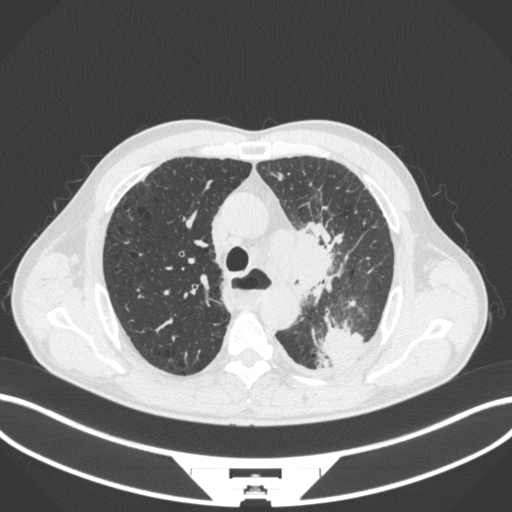
Chest CT, one axial slice; slice 274 of 411 in the series (ordered by position); reconstruction kernel B31f; lung window (W 1500 / L -600 HU); 1 mm slice thickness; 512 × 512 image matrix, field of view 400 × 400 mm. Patient: male, 57 years. Case-level facts recorded for this patient, not image findings: clinical TNM (as recorded): T2a N1 M0.
Outlined on this slice (rectangle marked by the reading radiologist):
- lung tumour (recorded histology: squamous cell carcinoma): bounding box [x1, y1, x2, y2] px = [262, 220, 337, 295]